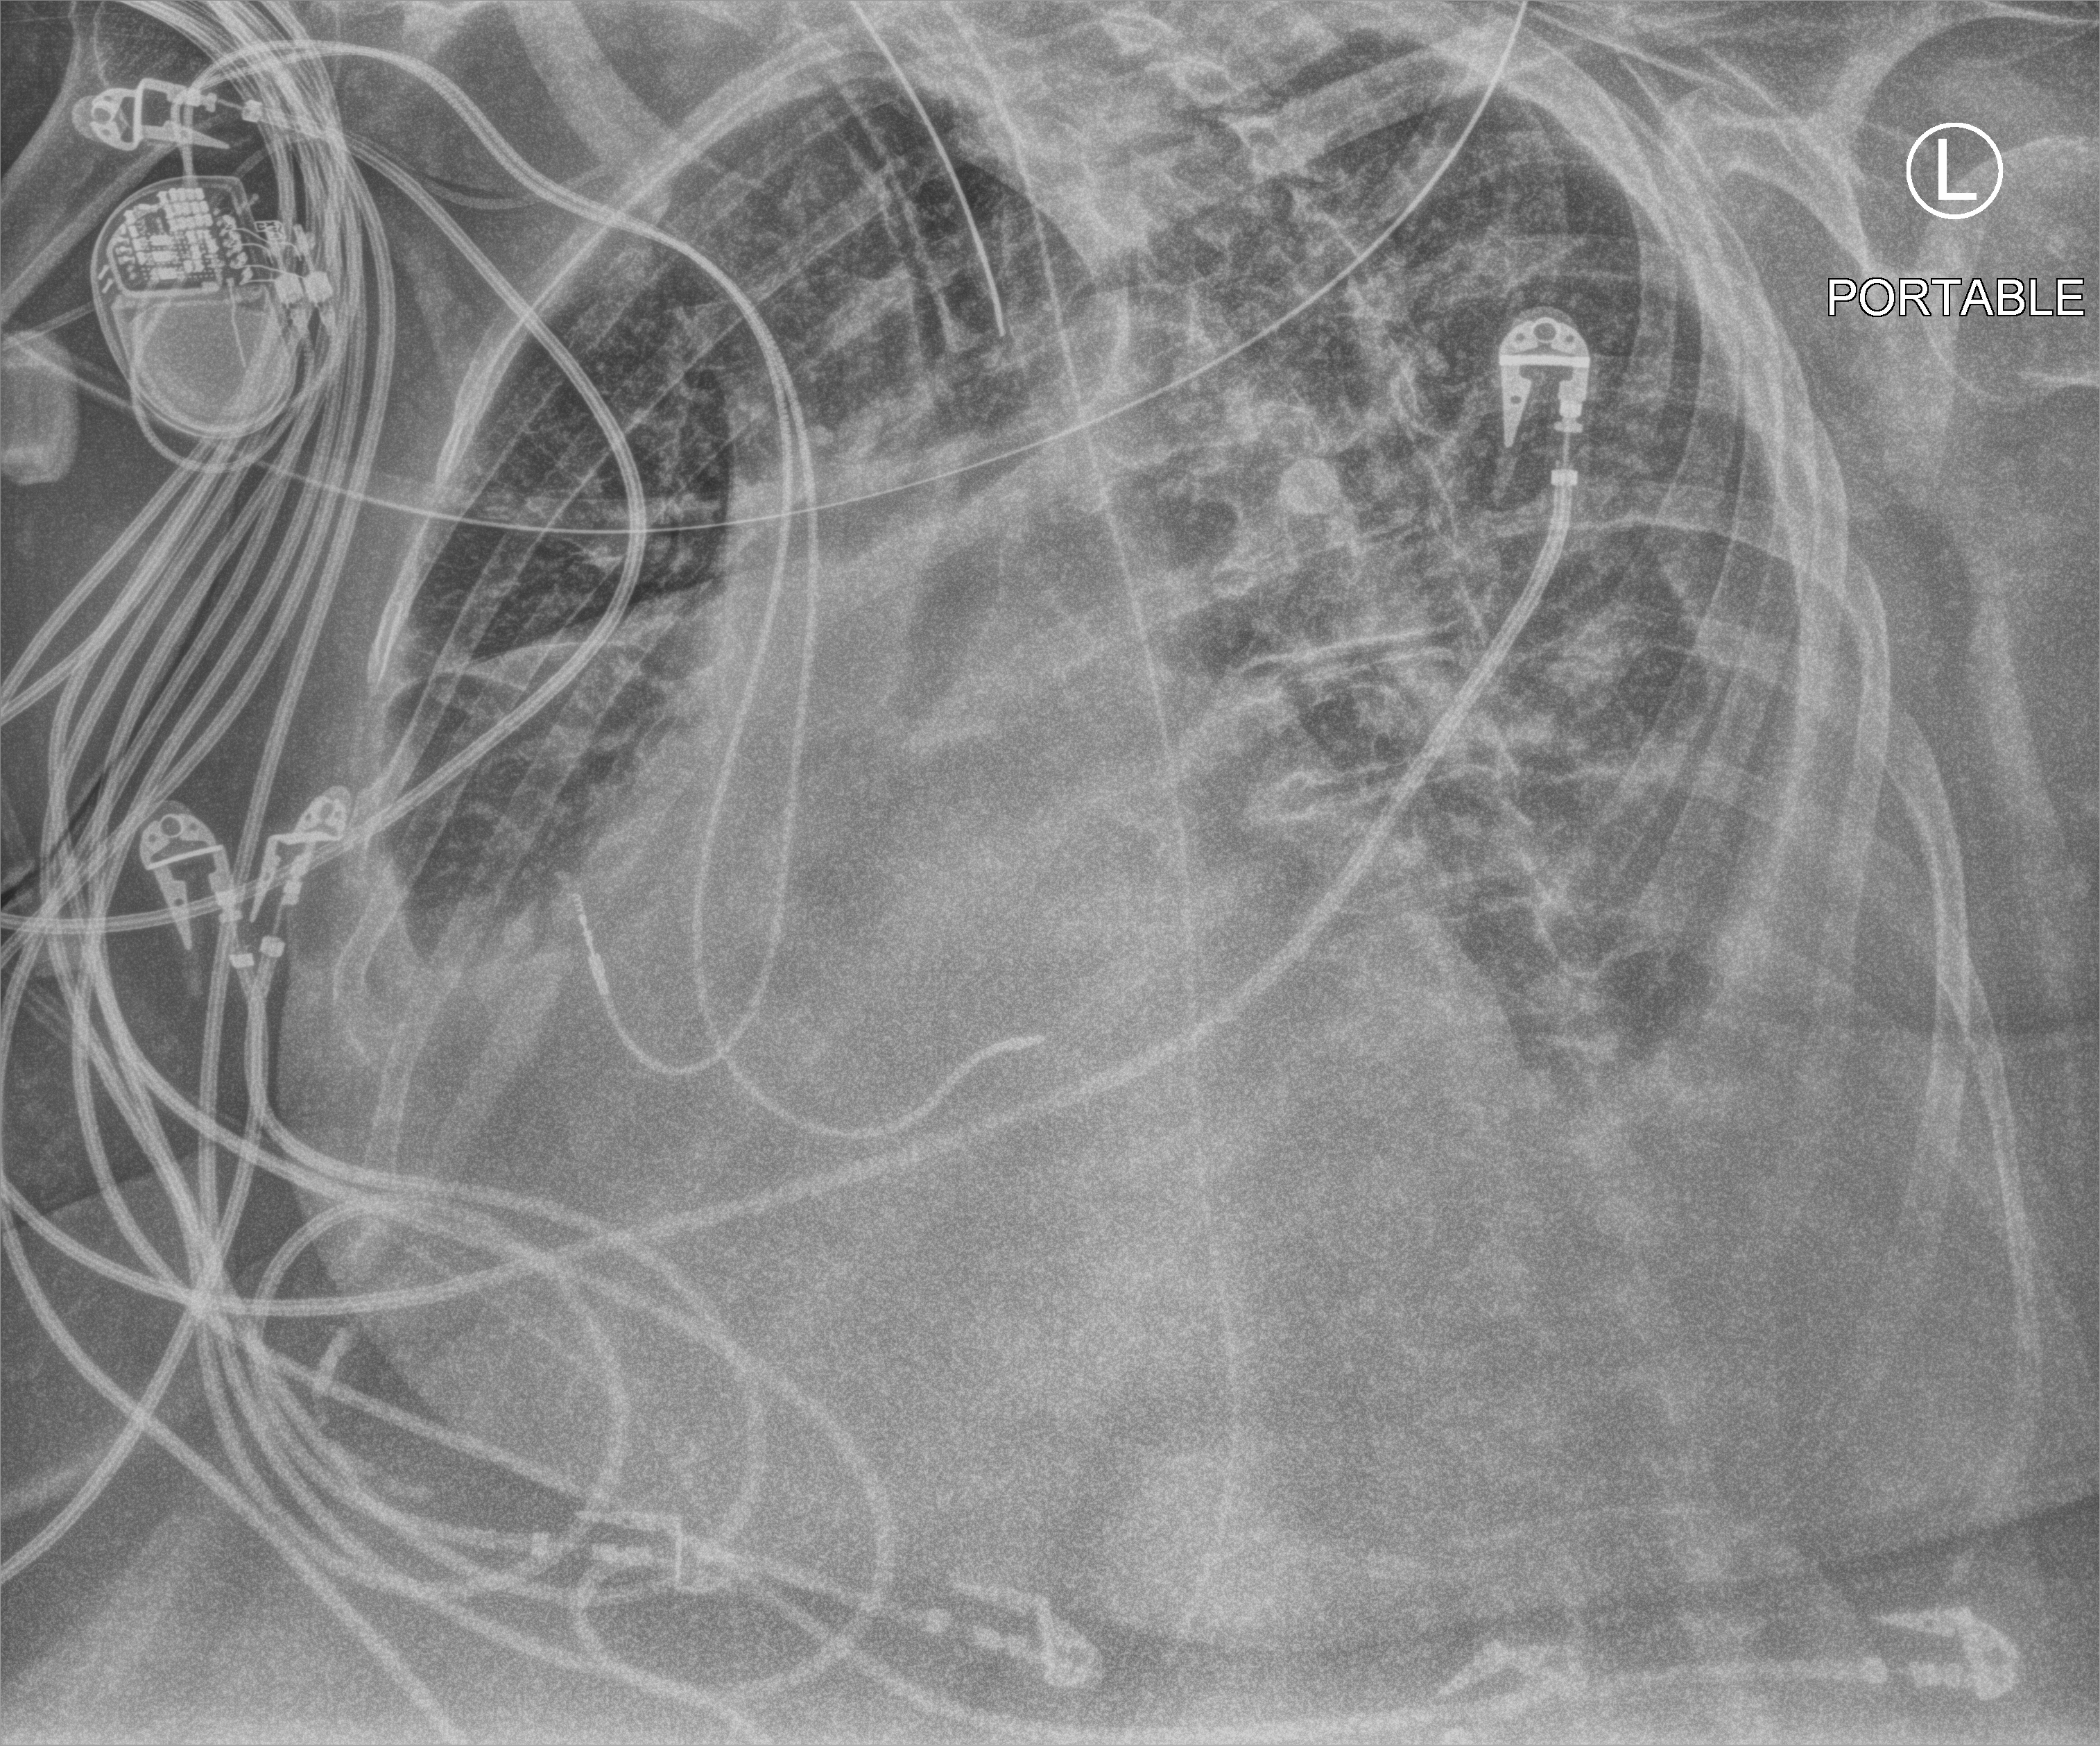
Portable chest radiograph, anteroposterior (AP) projection. Female patient hospitalised with COVID-19, age 75–90 years.
From the hospital-stay record, not from the radiograph (when in the stay this image was taken is not recorded):
- length of hospital stay: 21 days
- mechanically ventilated during this hospital stay: yes